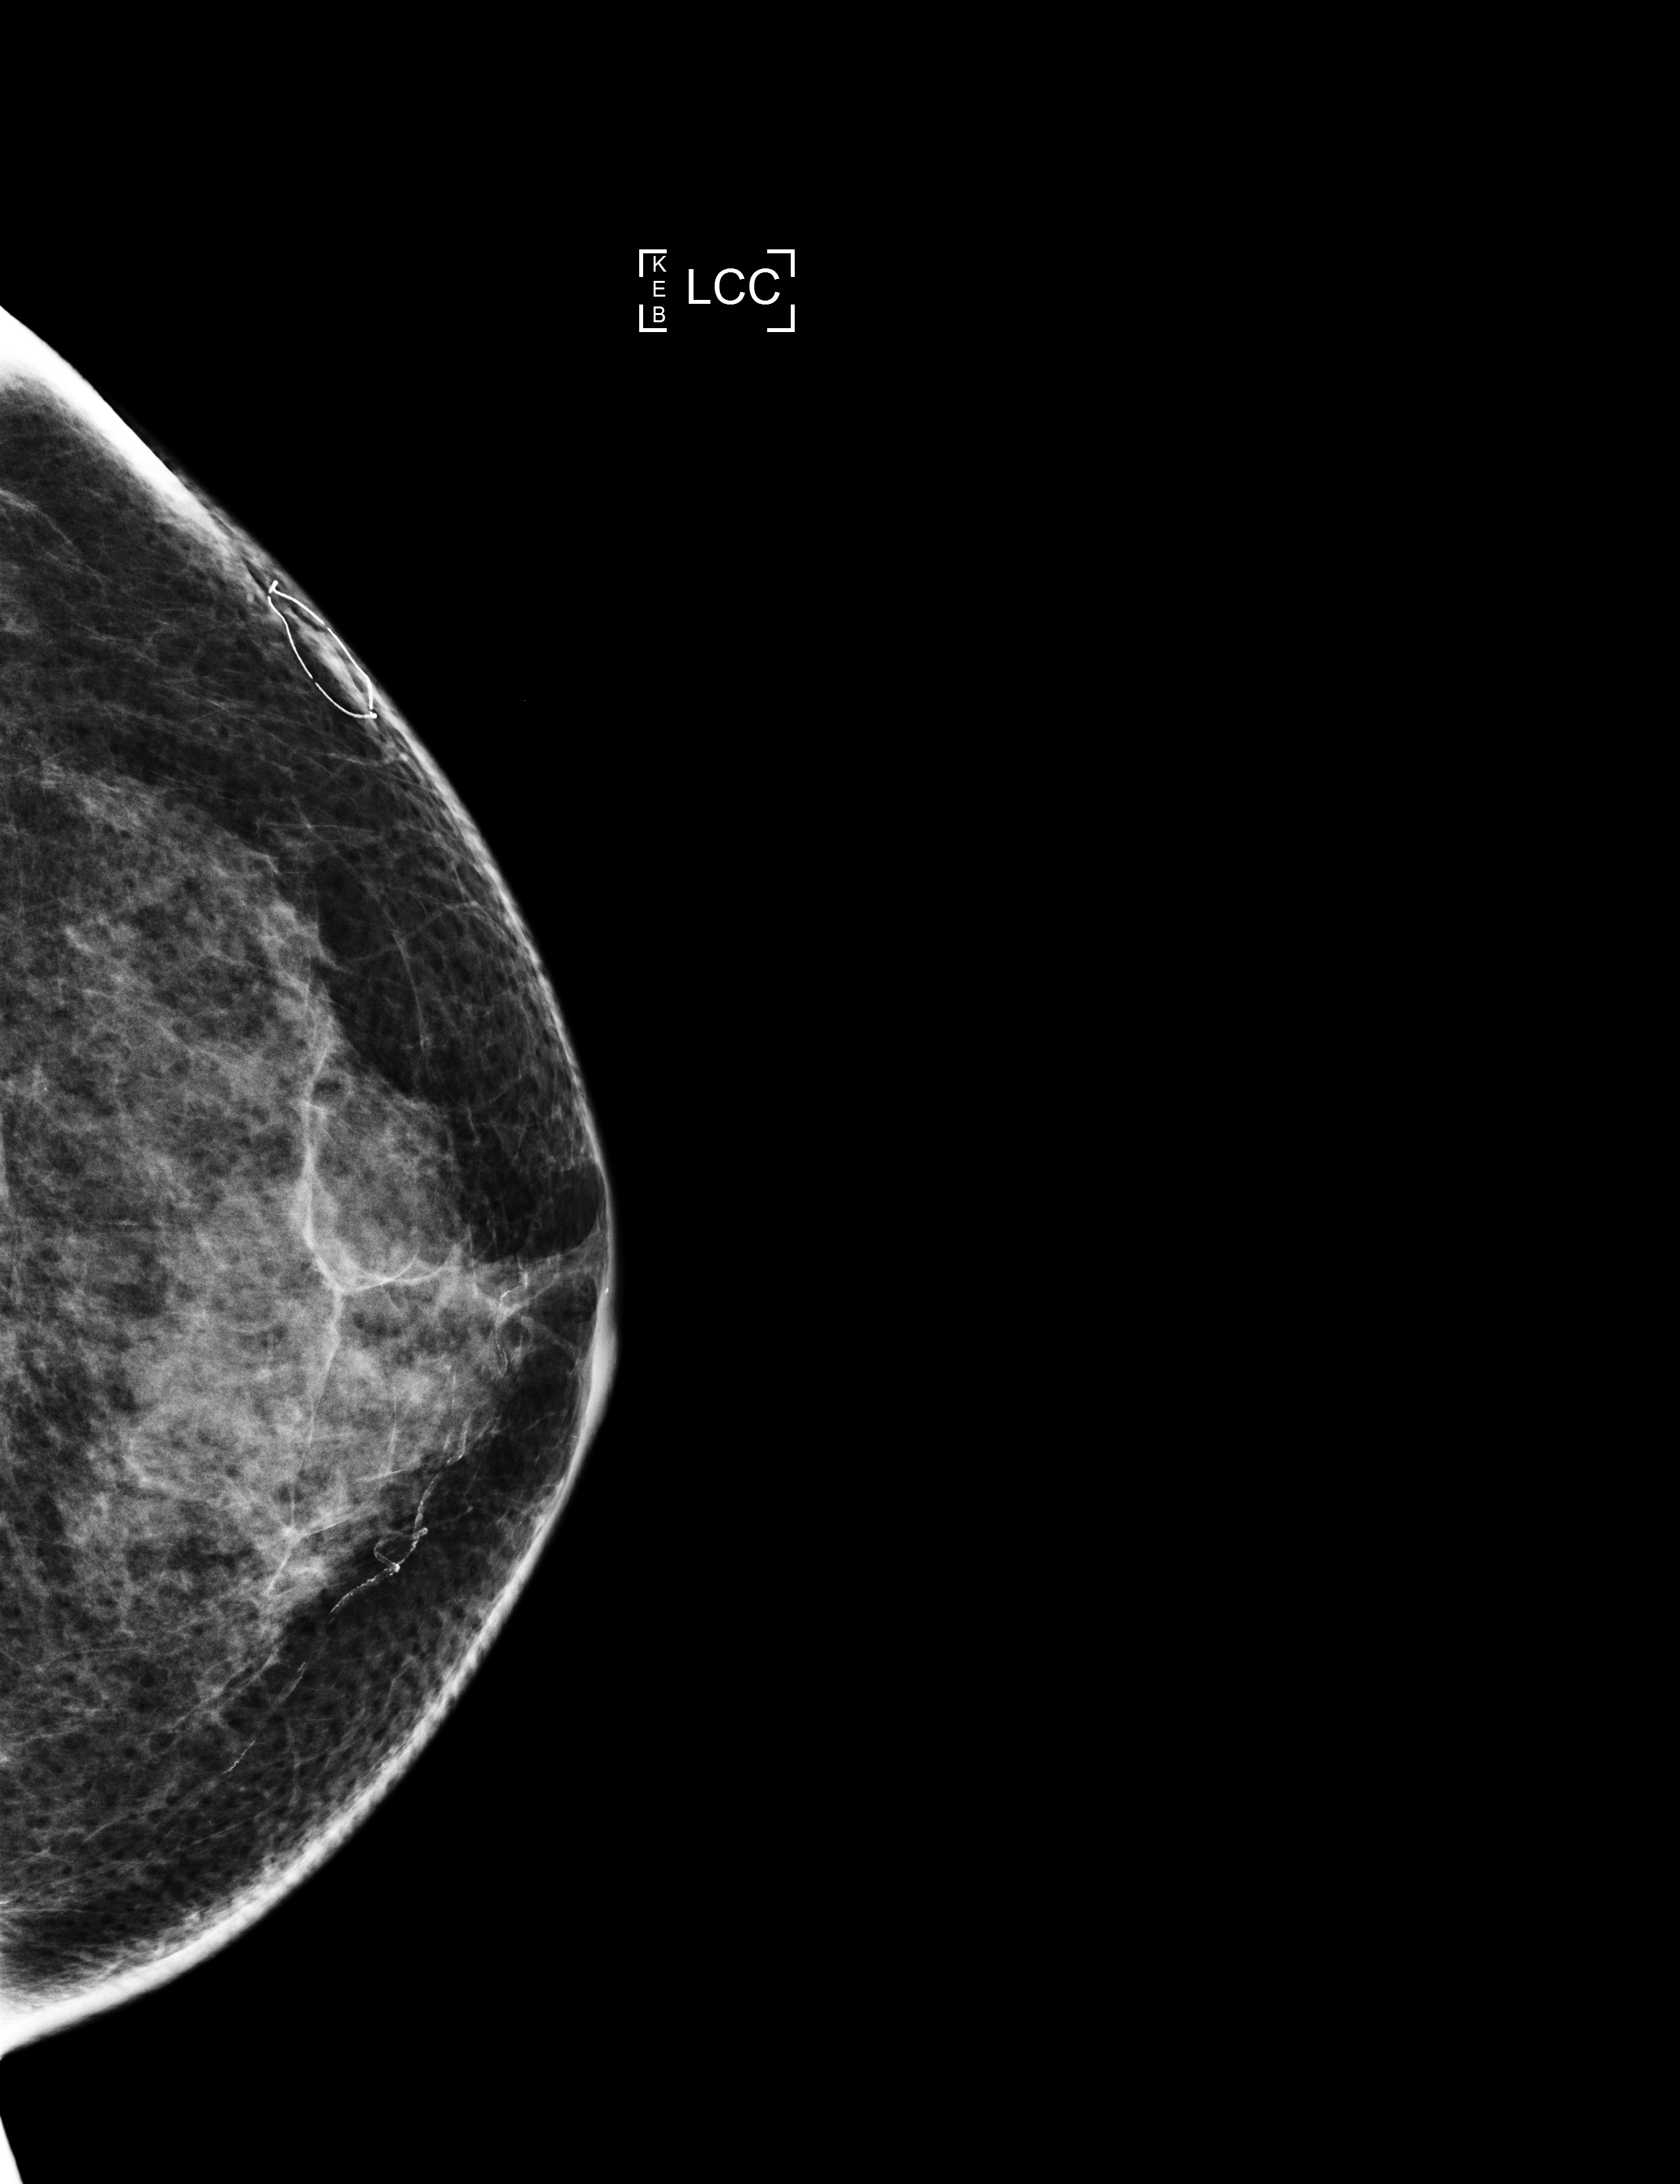
Annual screening mammography examination, system: Selenia Dimensions. Patient: female, 64 years.
Image type: full-field digital mammogram. Breast: left. Projection: craniocaudal (CC) view.